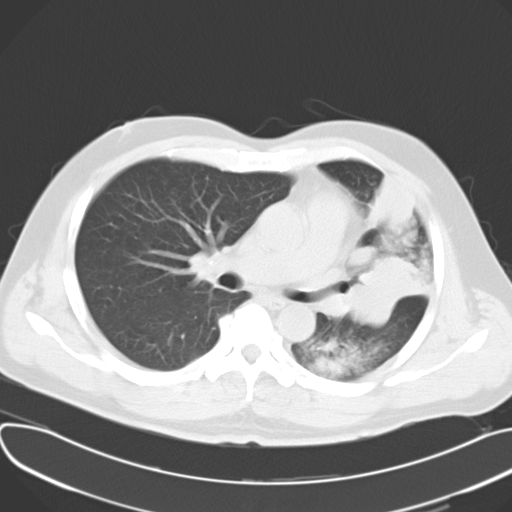
Chest CT, one axial slice; position 19 of 30 along the scan axis; 120 kVp; lung window (W 1500 / L -600 HU); 10 mm slice thickness; 512 × 512 image matrix, field of view 377 × 377 mm. Patient: male, 48 years. From the clinical record (not read from this slice): clinical TNM (as recorded): T4 N0 M0.
Structures marked on this image (bounding box drawn by a radiologist):
- lung tumour (recorded histology: adenocarcinoma): bounding box (x1, y1, x2, y2) in pixels: (347, 254, 428, 331)